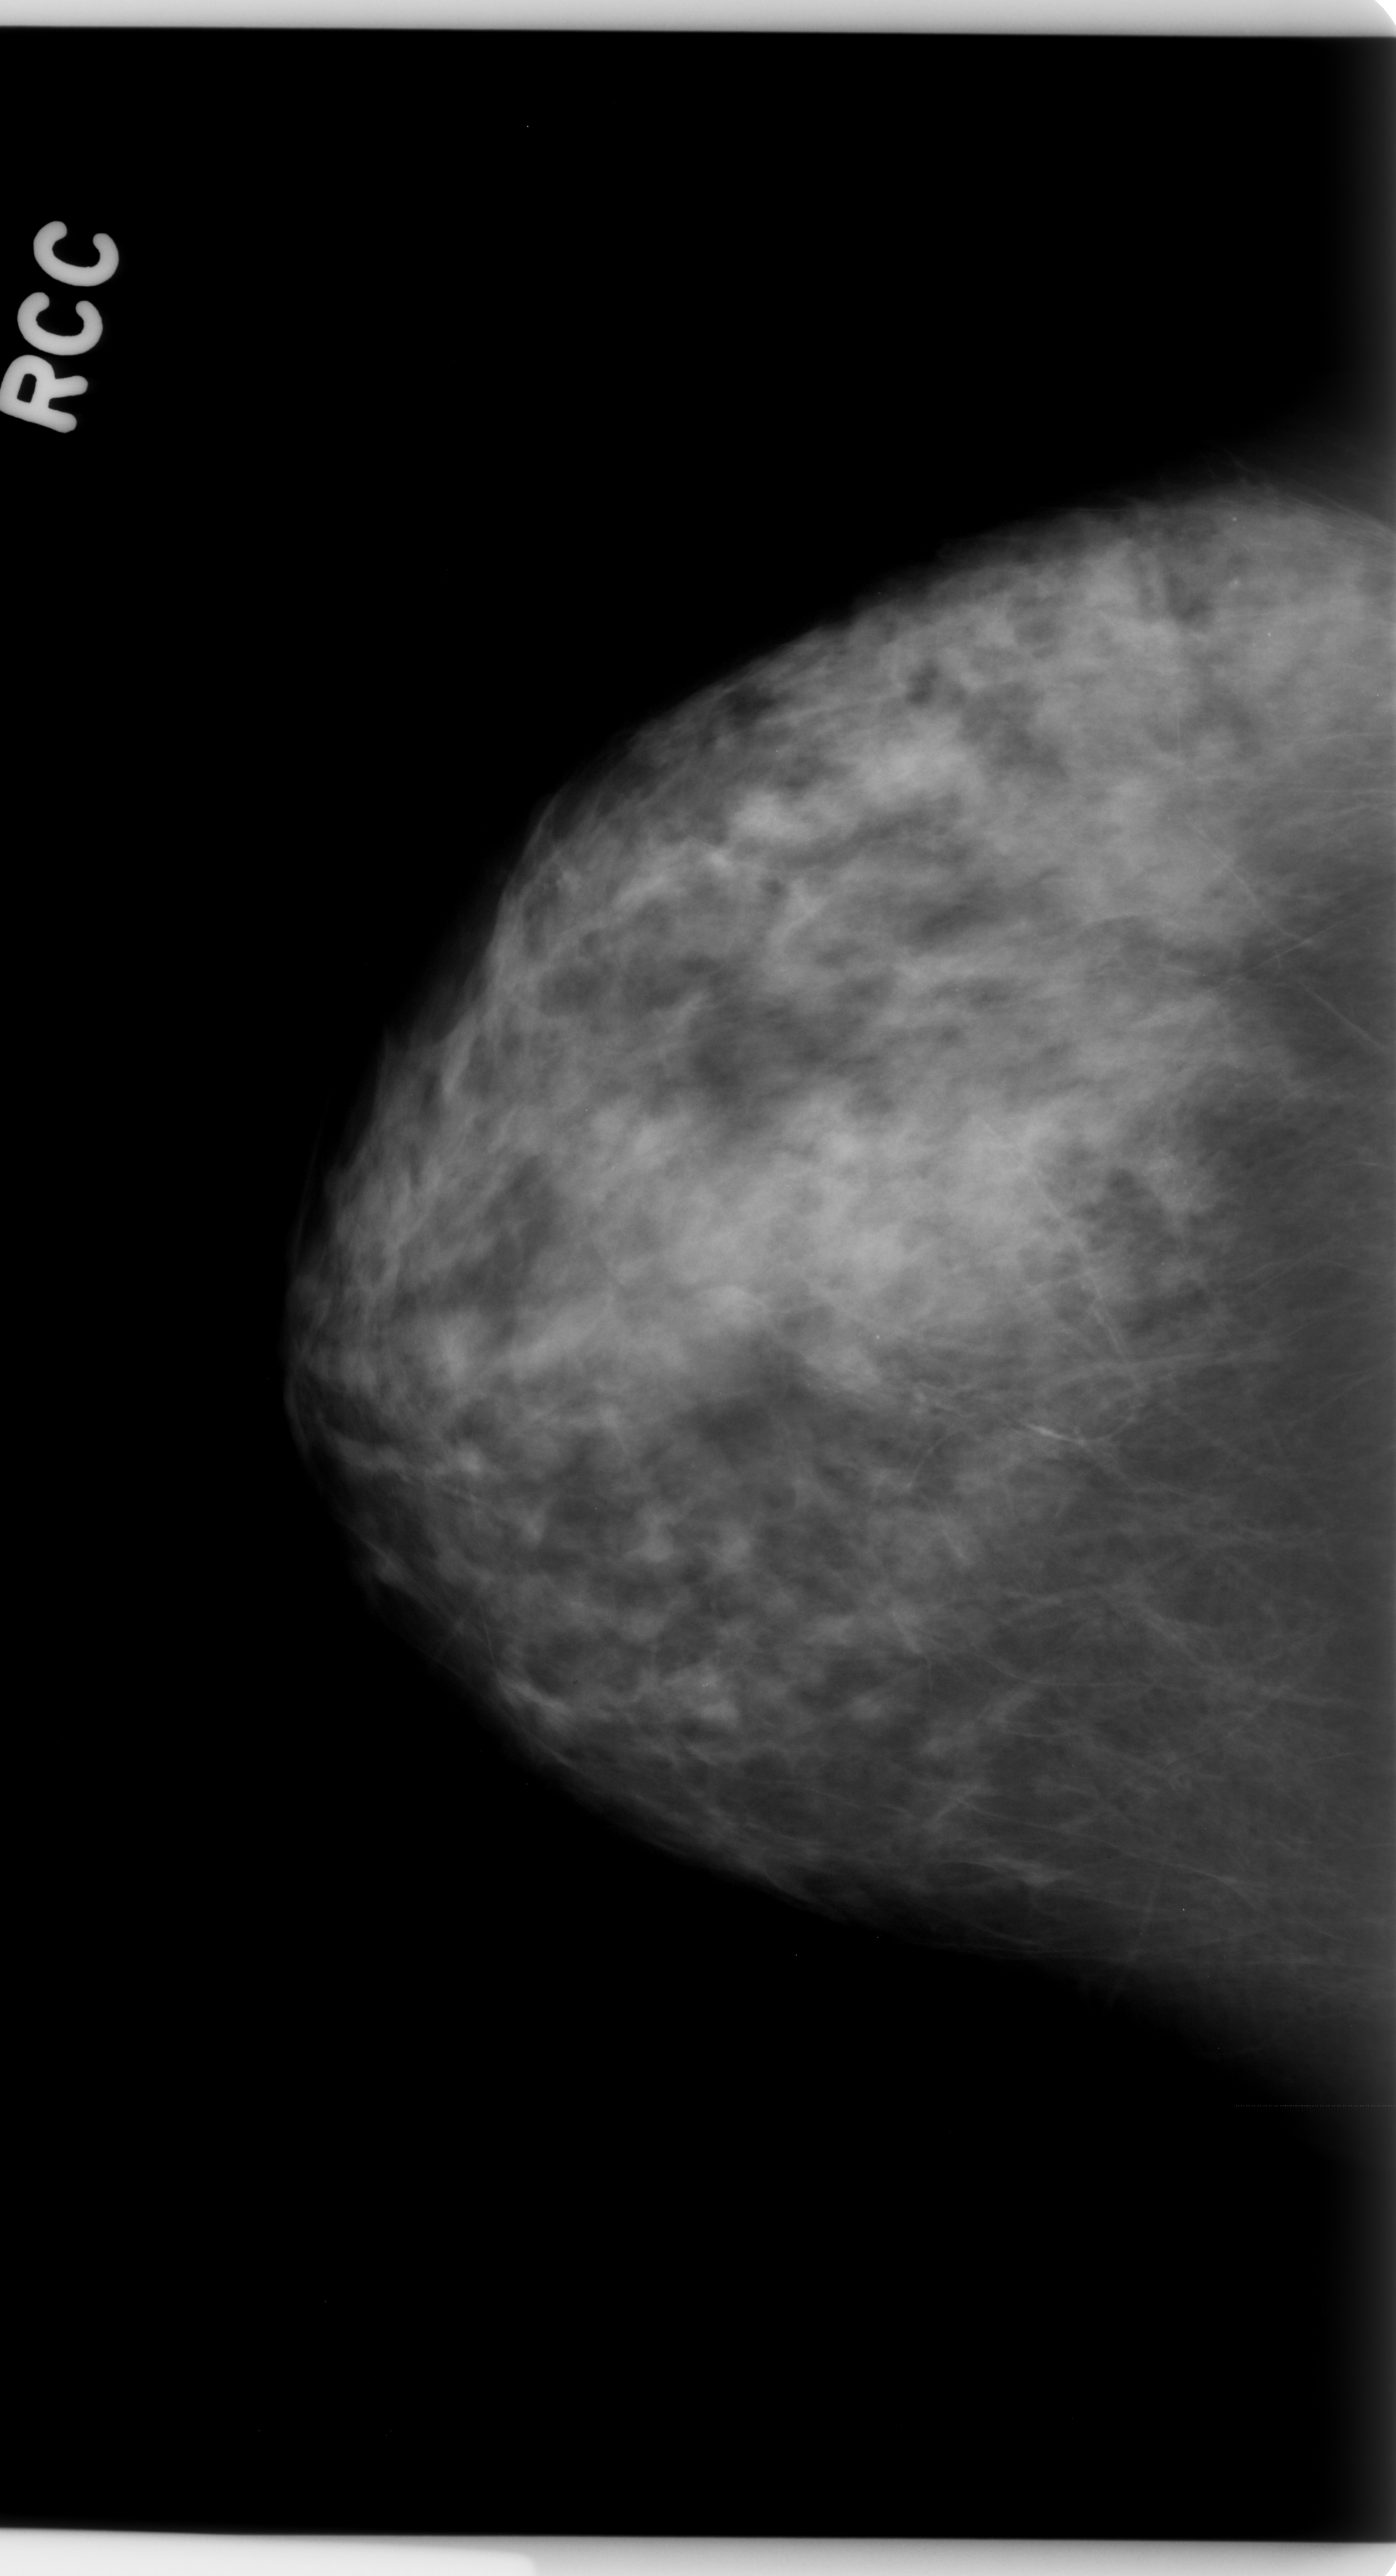
Scanned film-screen mammogram, right breast, craniocaudal (CC) view.
Calcifications, morphology amorphous, distribution clustered; BI-RADS assessment category 4; subtlety rating 2 on a 1 (subtle) to 5 (obvious) scale; pathology result (as recorded, not read from the image): benign.